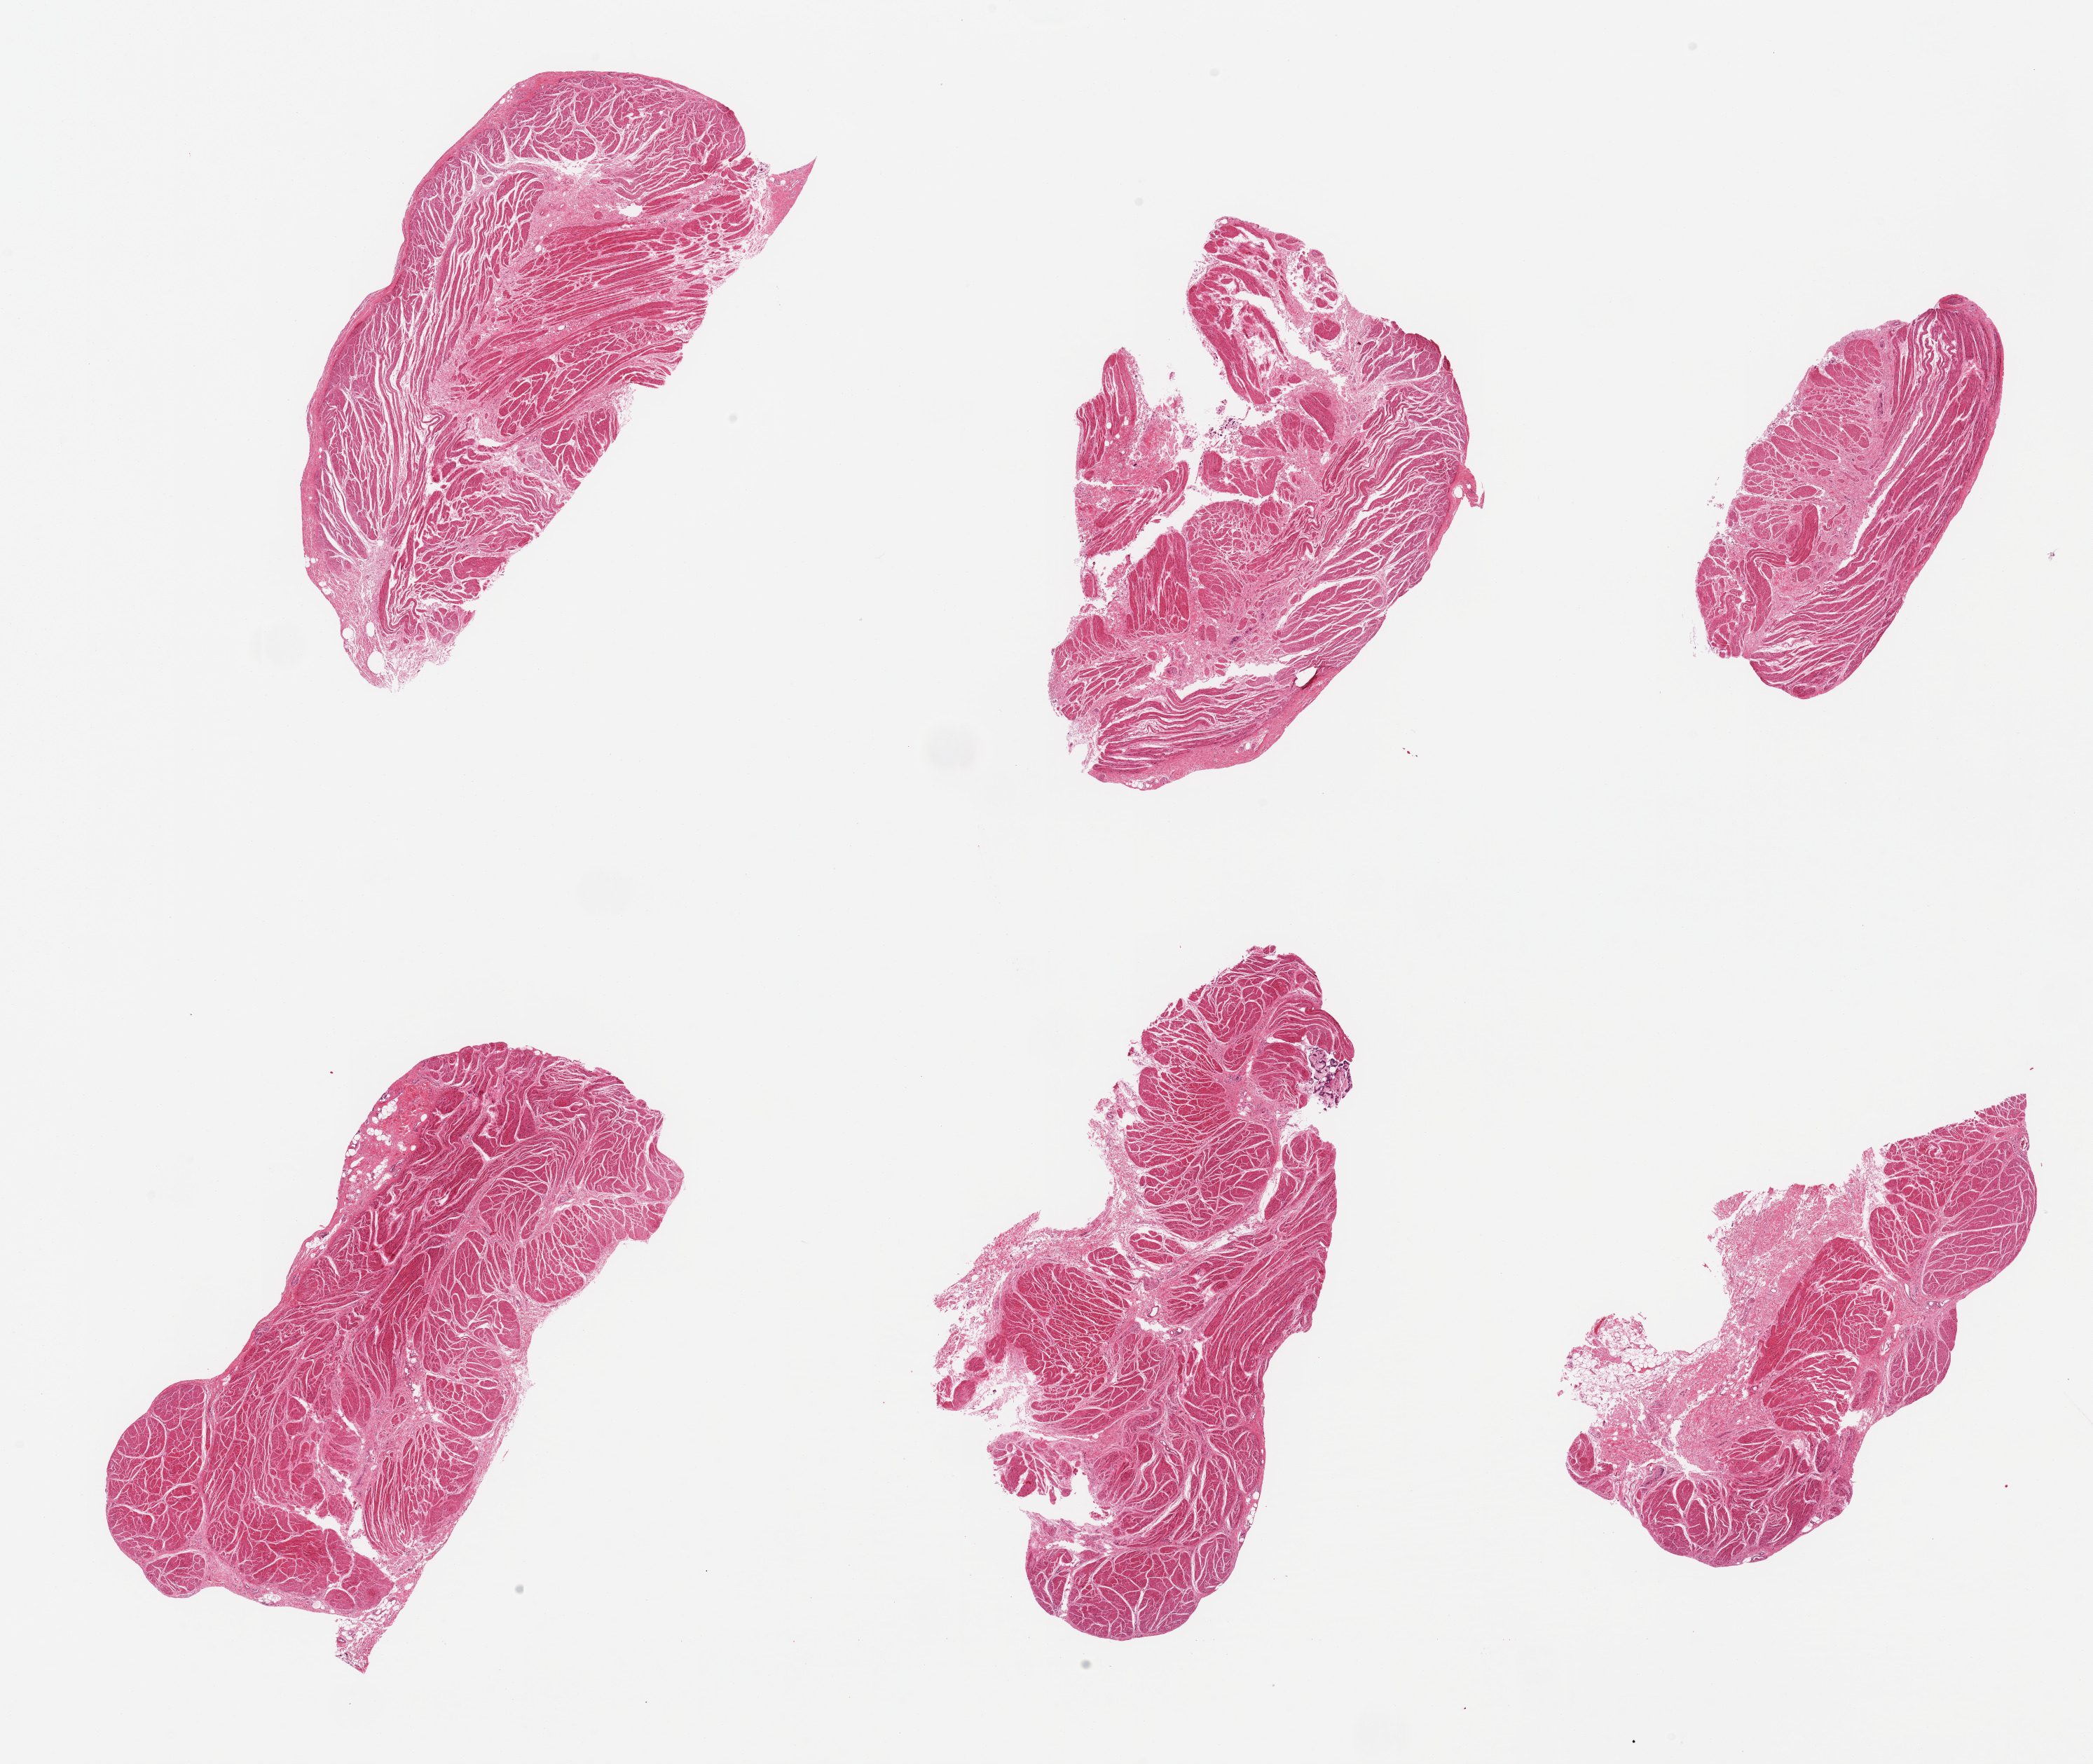
Digitized hematoxylin and eosin (H&E)-stained section, brightfield, a low-resolution overview of the entire scanned area, about 23.6 x 19.9 mm; PAXgene-fixed, paraffin-embedded tissue; target tissue: gastroesophageal junction; donor tissue sample. Donor sex: male.
Pathologist's review note for this sample: 6 pieces, confirmed target muscularis; focal adherent fibroadipose tisssue, ~1mm.